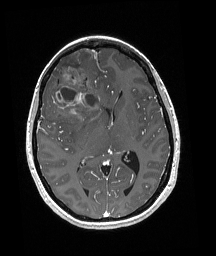
Brain MRI from a brain-tumour surgery series, one axial slice. Slice 96 of 192 in the series (ordered by position). T1-weighted post-contrast. 1 mm slice thickness. 216 × 256 image matrix, field of view 211 × 250 mm. Case-level facts recorded for this patient, not image findings: histopathology: Oligodendroglioma; WHO grade: 3; IDH mutation: yes; tumour location: Right Frontal.
Annotated regions visible in this slice (manually delineated by an expert):
- tumour: bounding box [x1, y1, x2, y2] px = [49, 58, 100, 118]